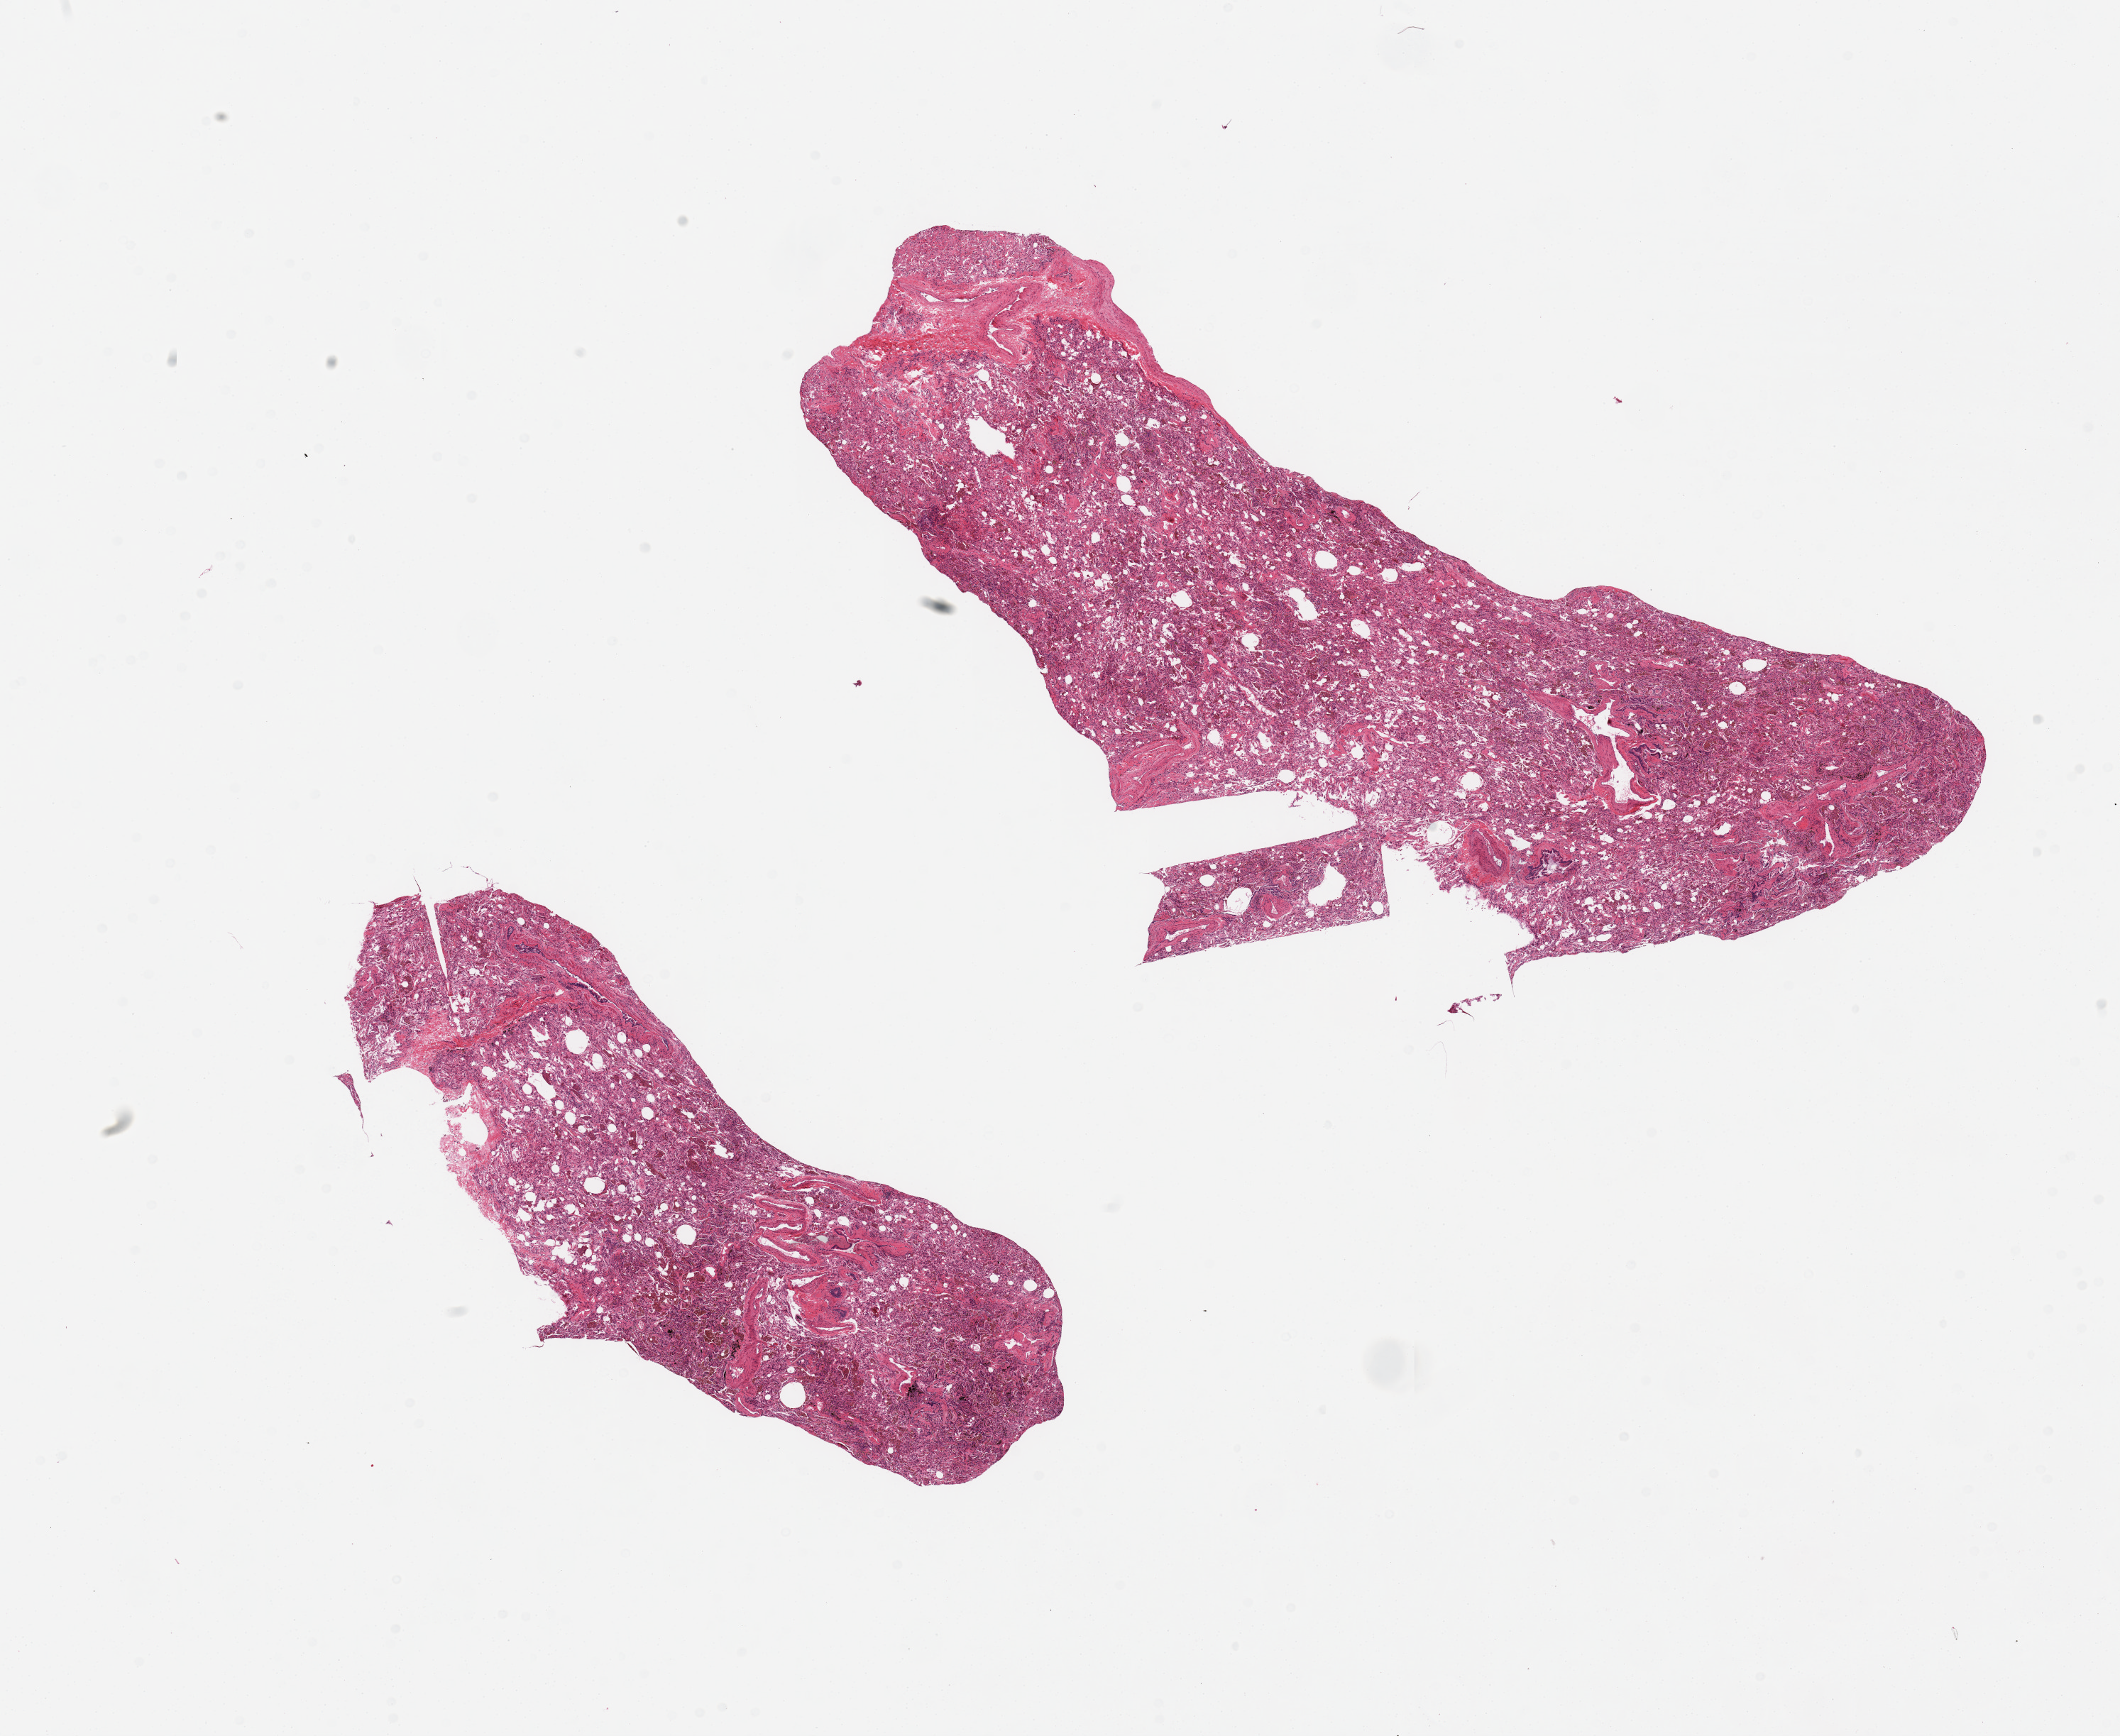
H&E whole-slide image, brightfield — shown as a low-resolution overview of the whole scanned area (about 23.6 x 19.3 mm), PAXgene-fixed paraffin-embedded (PFPE) section, sampled site (target tissue): lung, tissue donor sample. Female donor.
Reviewer comment on this tissue sample: 2 pieces; atelectasis, some fibrosis; numerous pigmented macrophages.